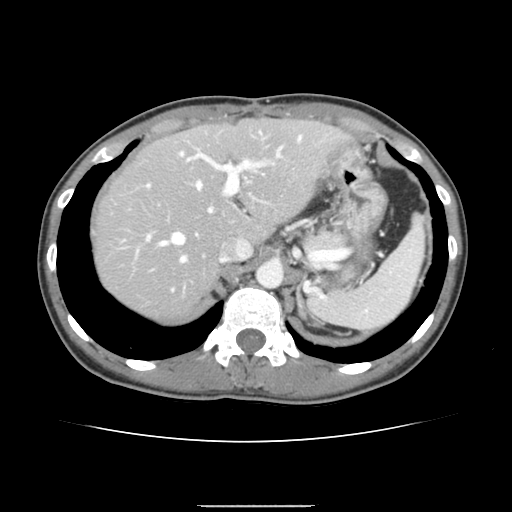
Contrast-enhanced abdominal CT, one axial slice. 120 kVp. Intravenous contrast given. Soft-tissue window (W 400 / L 40 HU). 512 × 512 image matrix, field of view 324 × 324 mm. Female patient, age 32 years. Case-level facts recorded for this patient, not image findings: diagnosis: colorectal cancer liver metastases, imaged before liver resection; multiple liver metastases: yes; largest metastasis: 0.7 cm; chemotherapy before resection: yes.
Outlined on this slice (expert manual segmentation):
- hepatic veins: box from (x=157, y=151) to (x=280, y=262) px
- liver: (x=95, y=120)–(x=344, y=320)
- planned liver remnant (the part of the liver to remain after resection): (x=94, y=120)–(x=345, y=278)
- portal vein (with intrahepatic branches): (x=147, y=132)–(x=302, y=290)